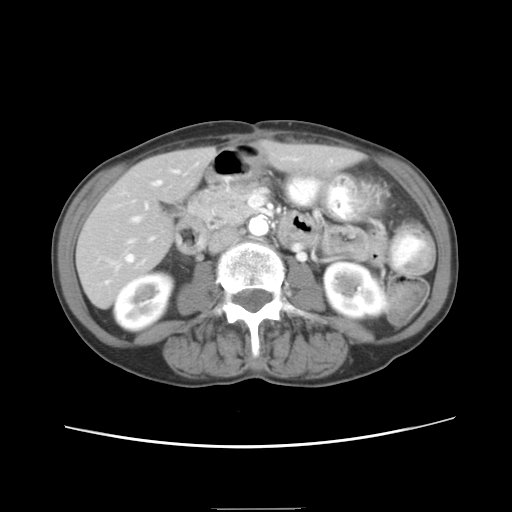
Contrast-enhanced abdominal CT, one axial slice; position 6 of 26 along the scan axis; reconstruction kernel STANDARD; 120 kVp; soft-tissue window (W 400 / L 40 HU); 7.5 mm slice thickness; 512 × 512 image matrix. Female patient, age 65 years. Case-level facts recorded for this patient, not image findings: diagnosis: colorectal cancer liver metastases, imaged before liver resection; multiple liver metastases: no; disease in both lobes: yes; chemotherapy before resection: yes.
Structures marked on this image (expert manual segmentation):
- hepatic veins: bounding box <109,158,298,269> (left, top, right, bottom; pixels)
- liver: <77,147,353,306>
- planned liver remnant (the part of the liver to remain after resection): <80,147,353,305>
- portal vein (with intrahepatic branches): <133,169,178,221>